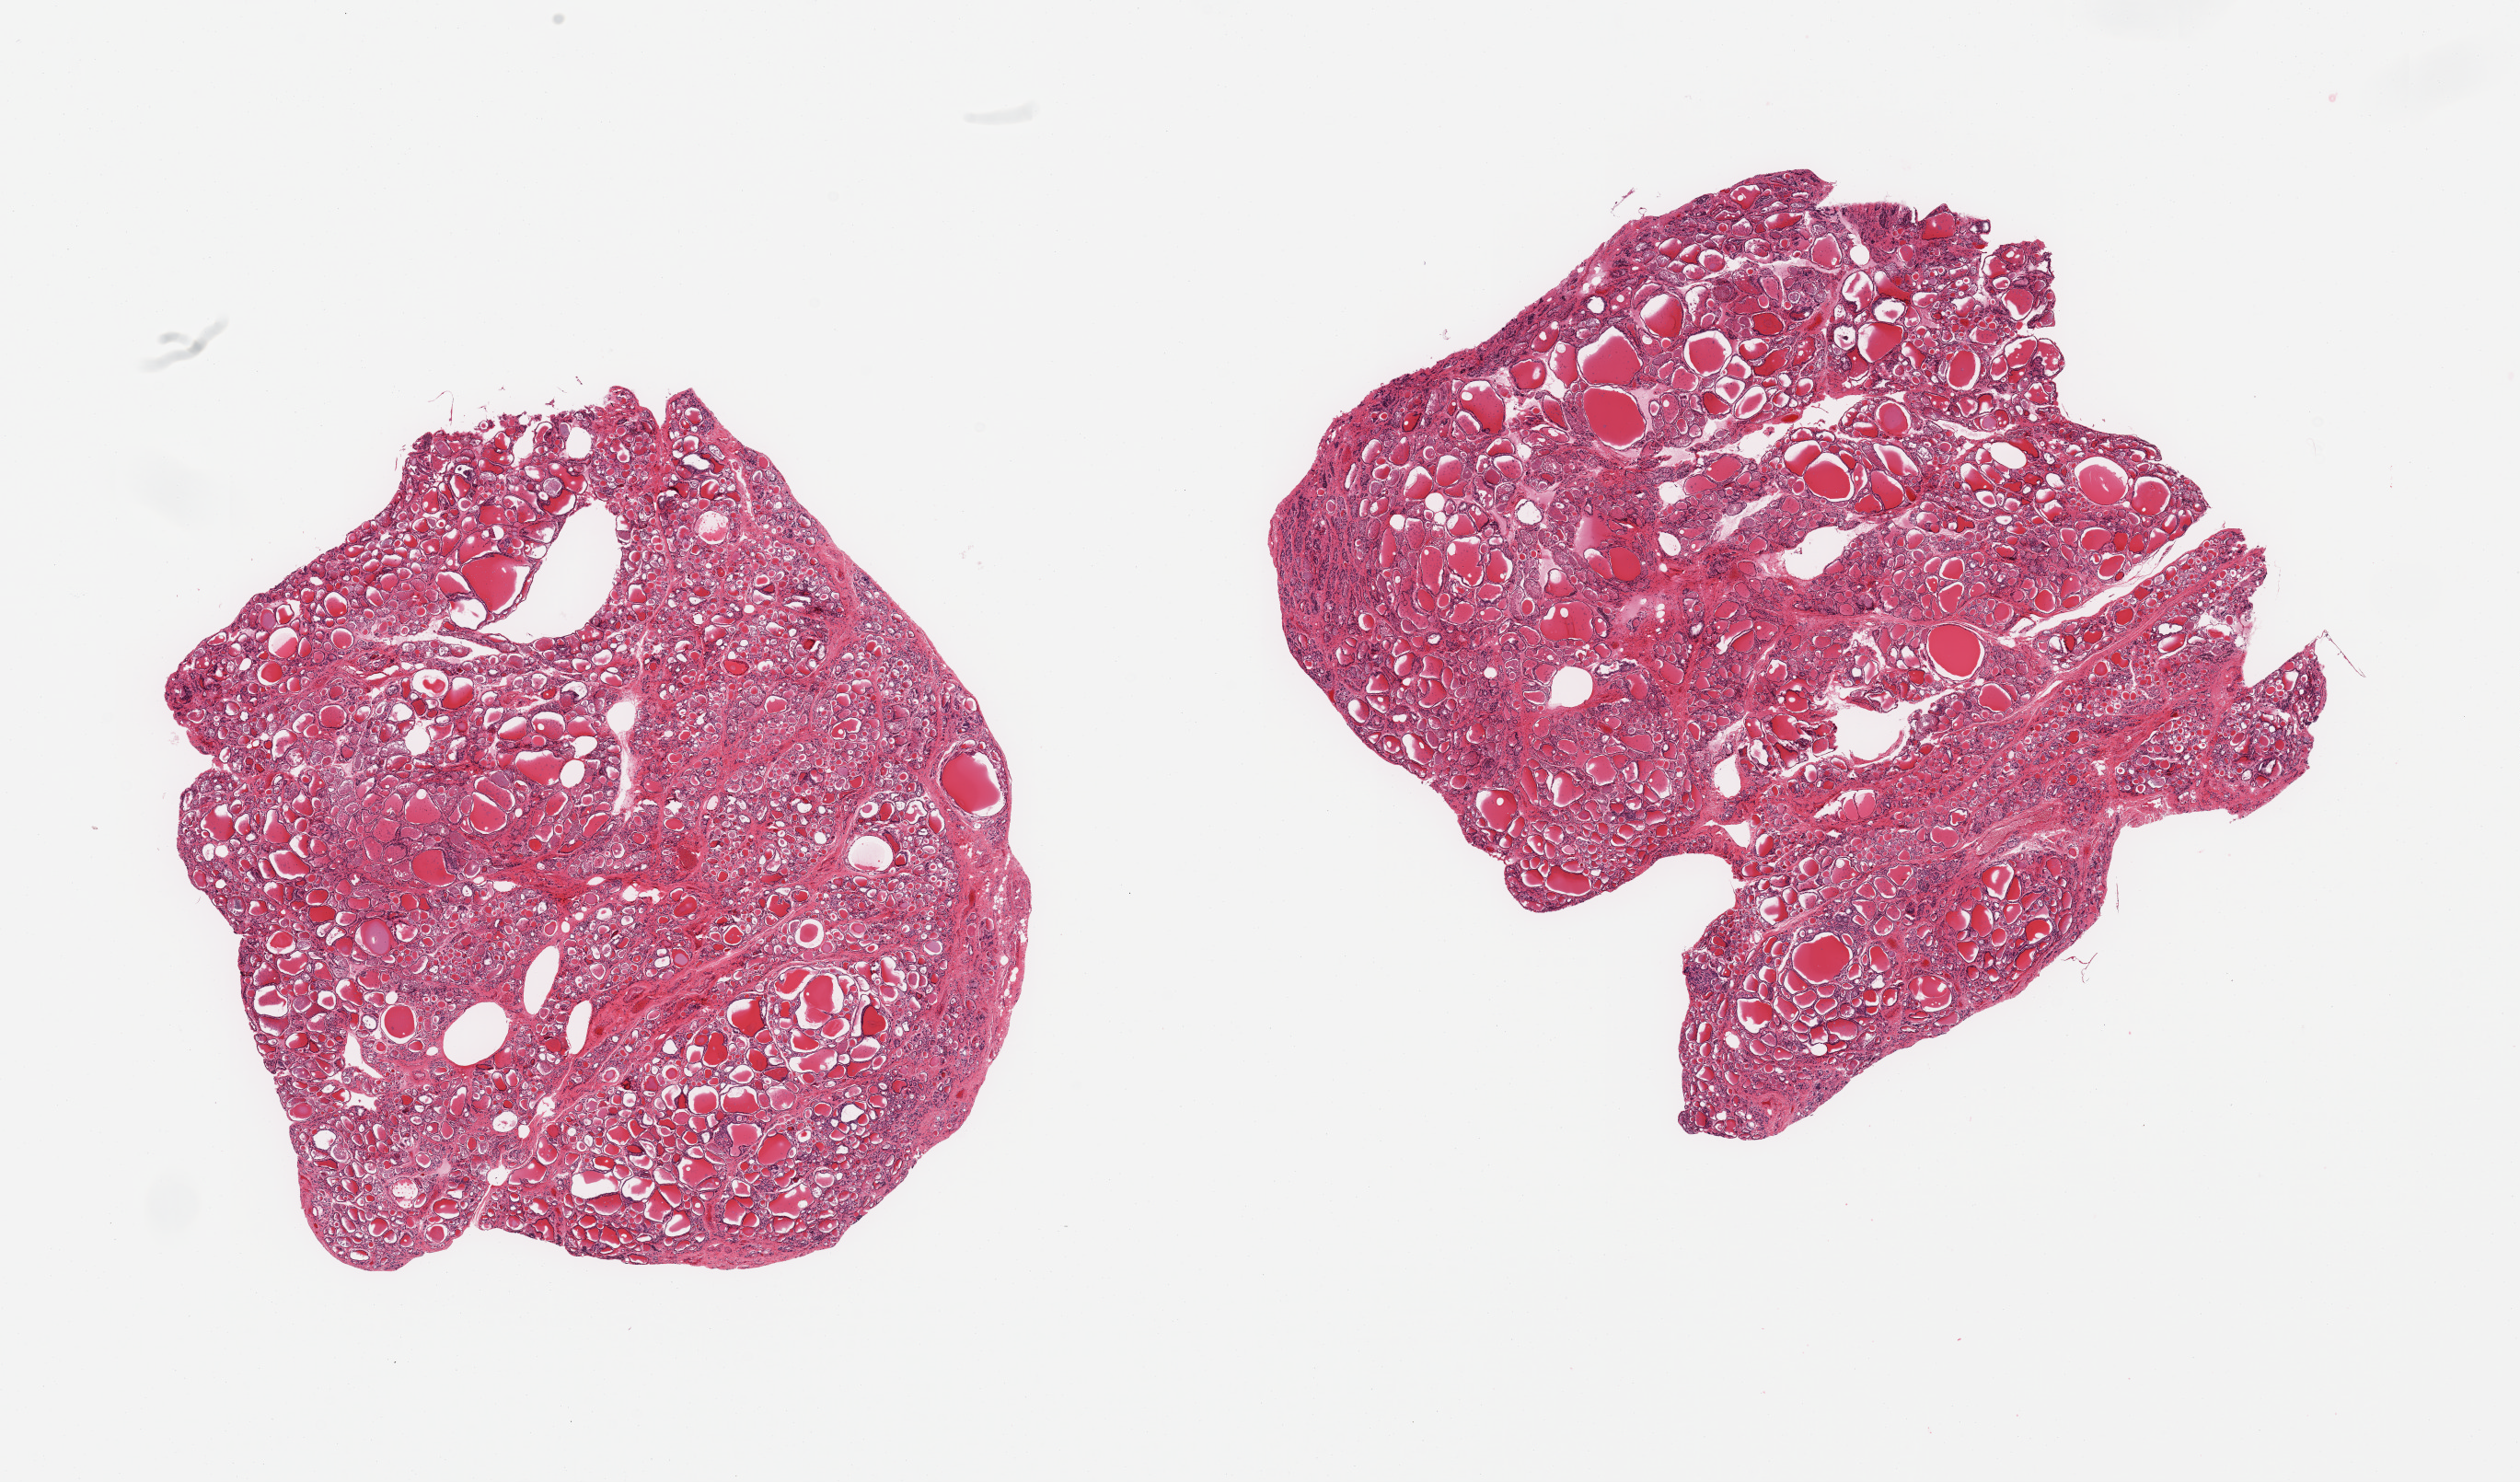
Hematoxylin and eosin (H&E) whole-slide image, brightfield — low-resolution overview of the scanned area, about 21.7 x 12.7 mm; PAXgene-fixed paraffin-embedded (PFPE) section; sampled site (target tissue): thyroid; donor tissue sample. Donor sex: female.
Reviewer comment on this tissue sample: 2 pieces; no lesions.